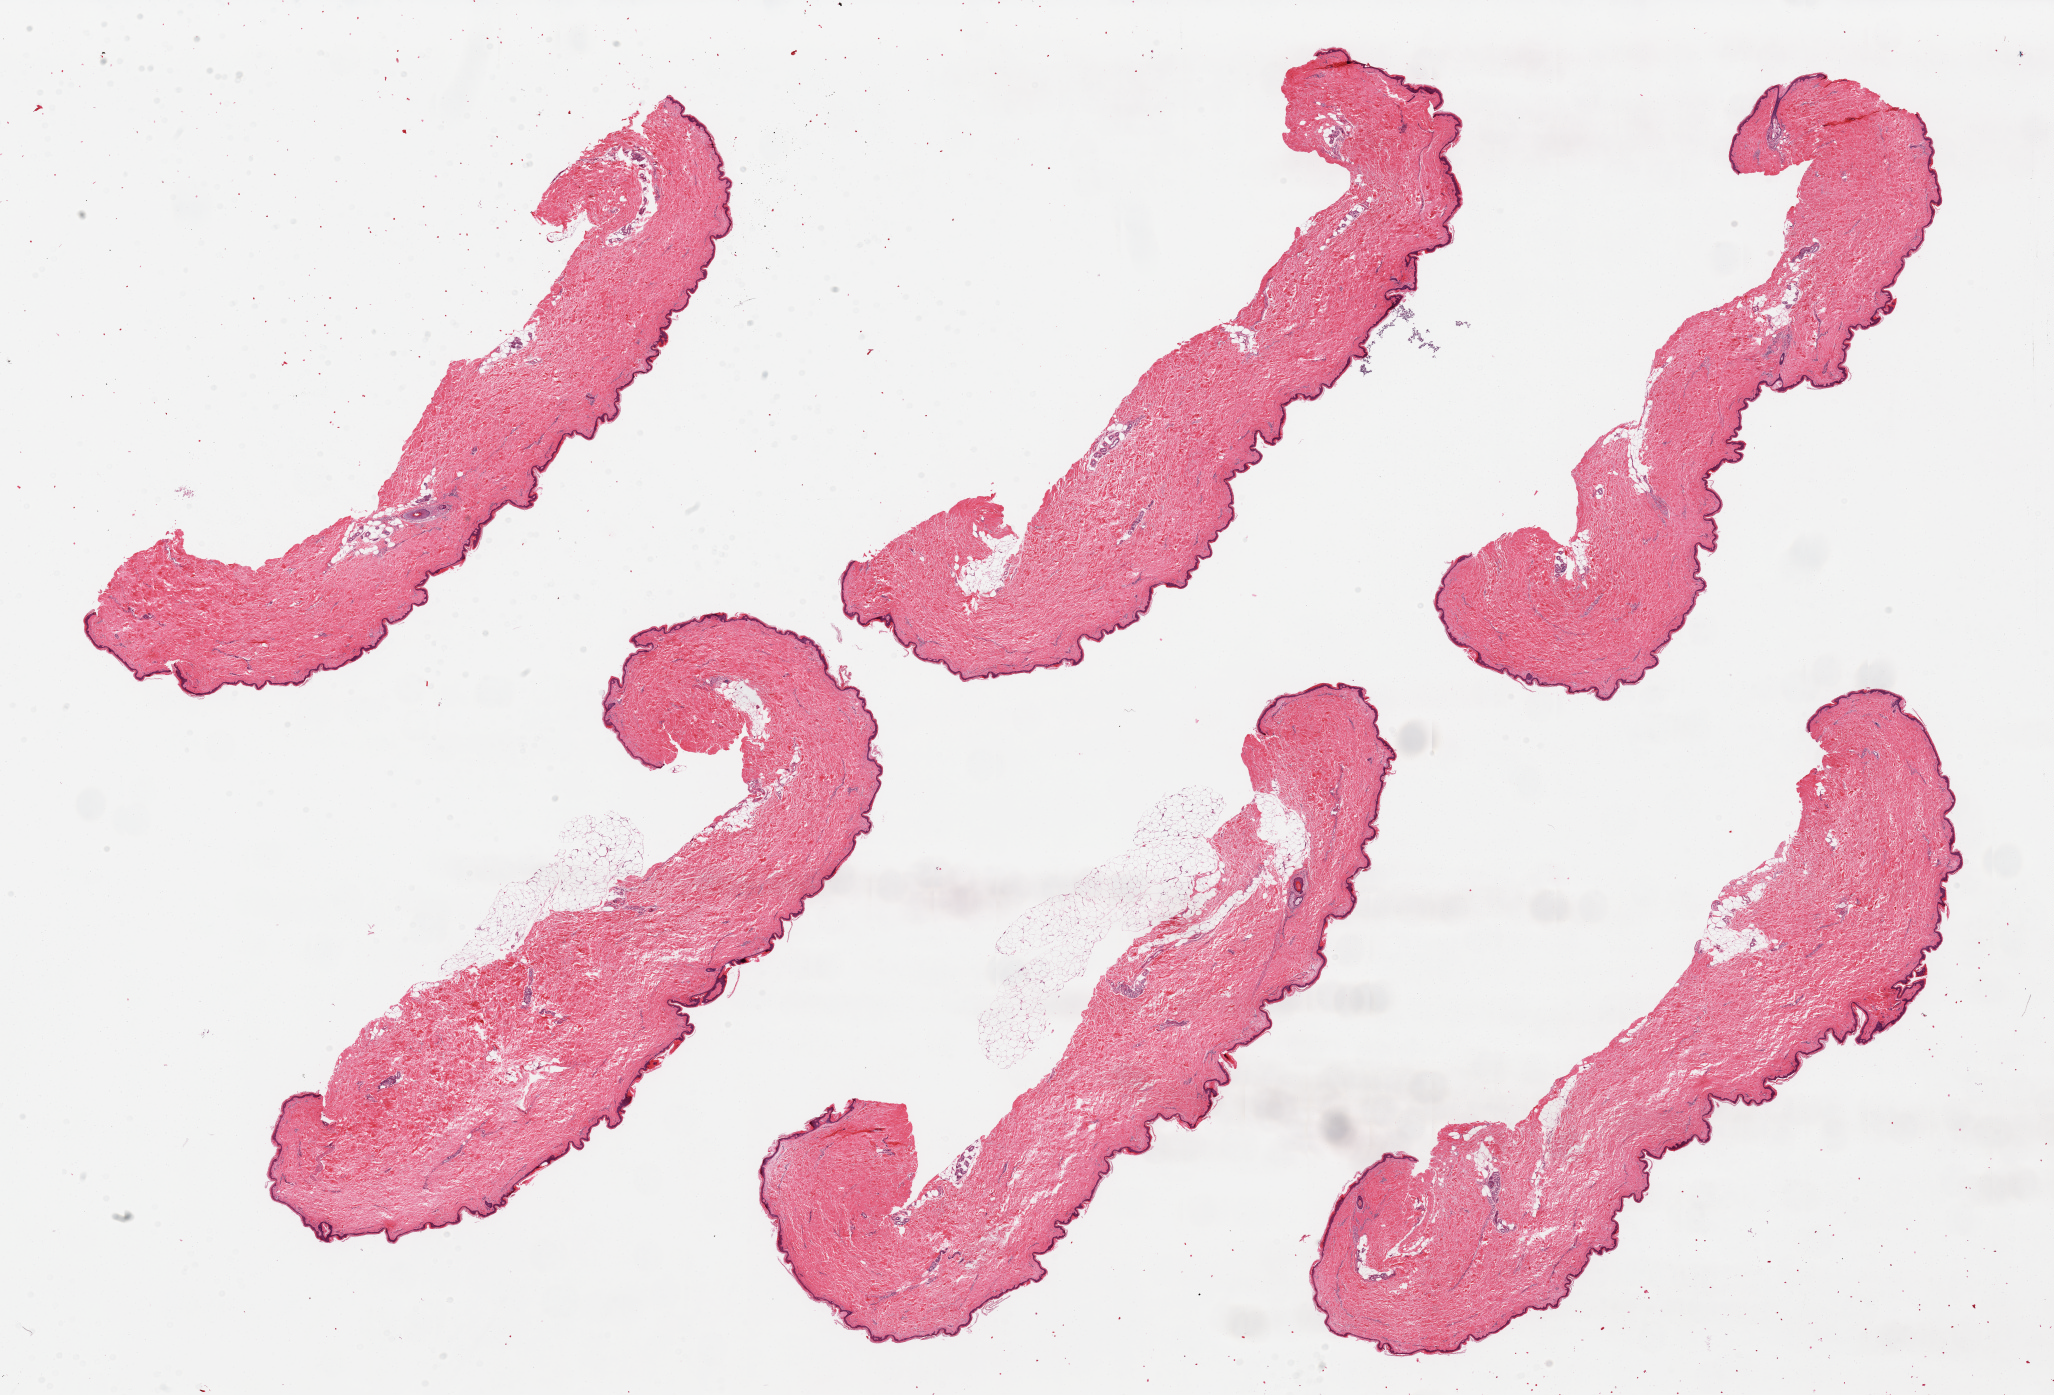
Whole-slide image, hematoxylin and eosin (H&E) stain, shown as a low-resolution overview of the whole scanned area (about 32.5 x 22.1 mm); PAXgene-fixed, paraffin-embedded tissue; sampled site (target tissue): skin of suprapubic region; donor tissue sample. Donor sex: male.
Pathologist's review note for this sample: 6 pieces, 2 pieces have ~15% attached adipose tissue.